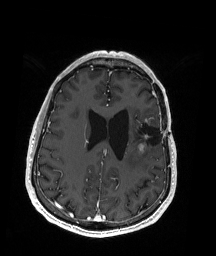
Brain MRI from a brain-tumour surgery series, one axial slice. Slice 70 of 192 in the series (ordered by position). T1-weighted post-contrast. 1 mm slice thickness. 216 × 256 image matrix, field of view 211 × 250 mm. From the clinical record (not read from this slice): histopathology: Oligodendroglioma; WHO grade: 2; IDH mutation: yes; tumour location: Left Insular.
Annotated regions visible in this slice (outlined manually by an expert reader):
- previous resection cavity: bounding box (x1, y1, x2, y2) in pixels: (132, 121, 163, 148)
- tumour: (137, 117, 153, 153)